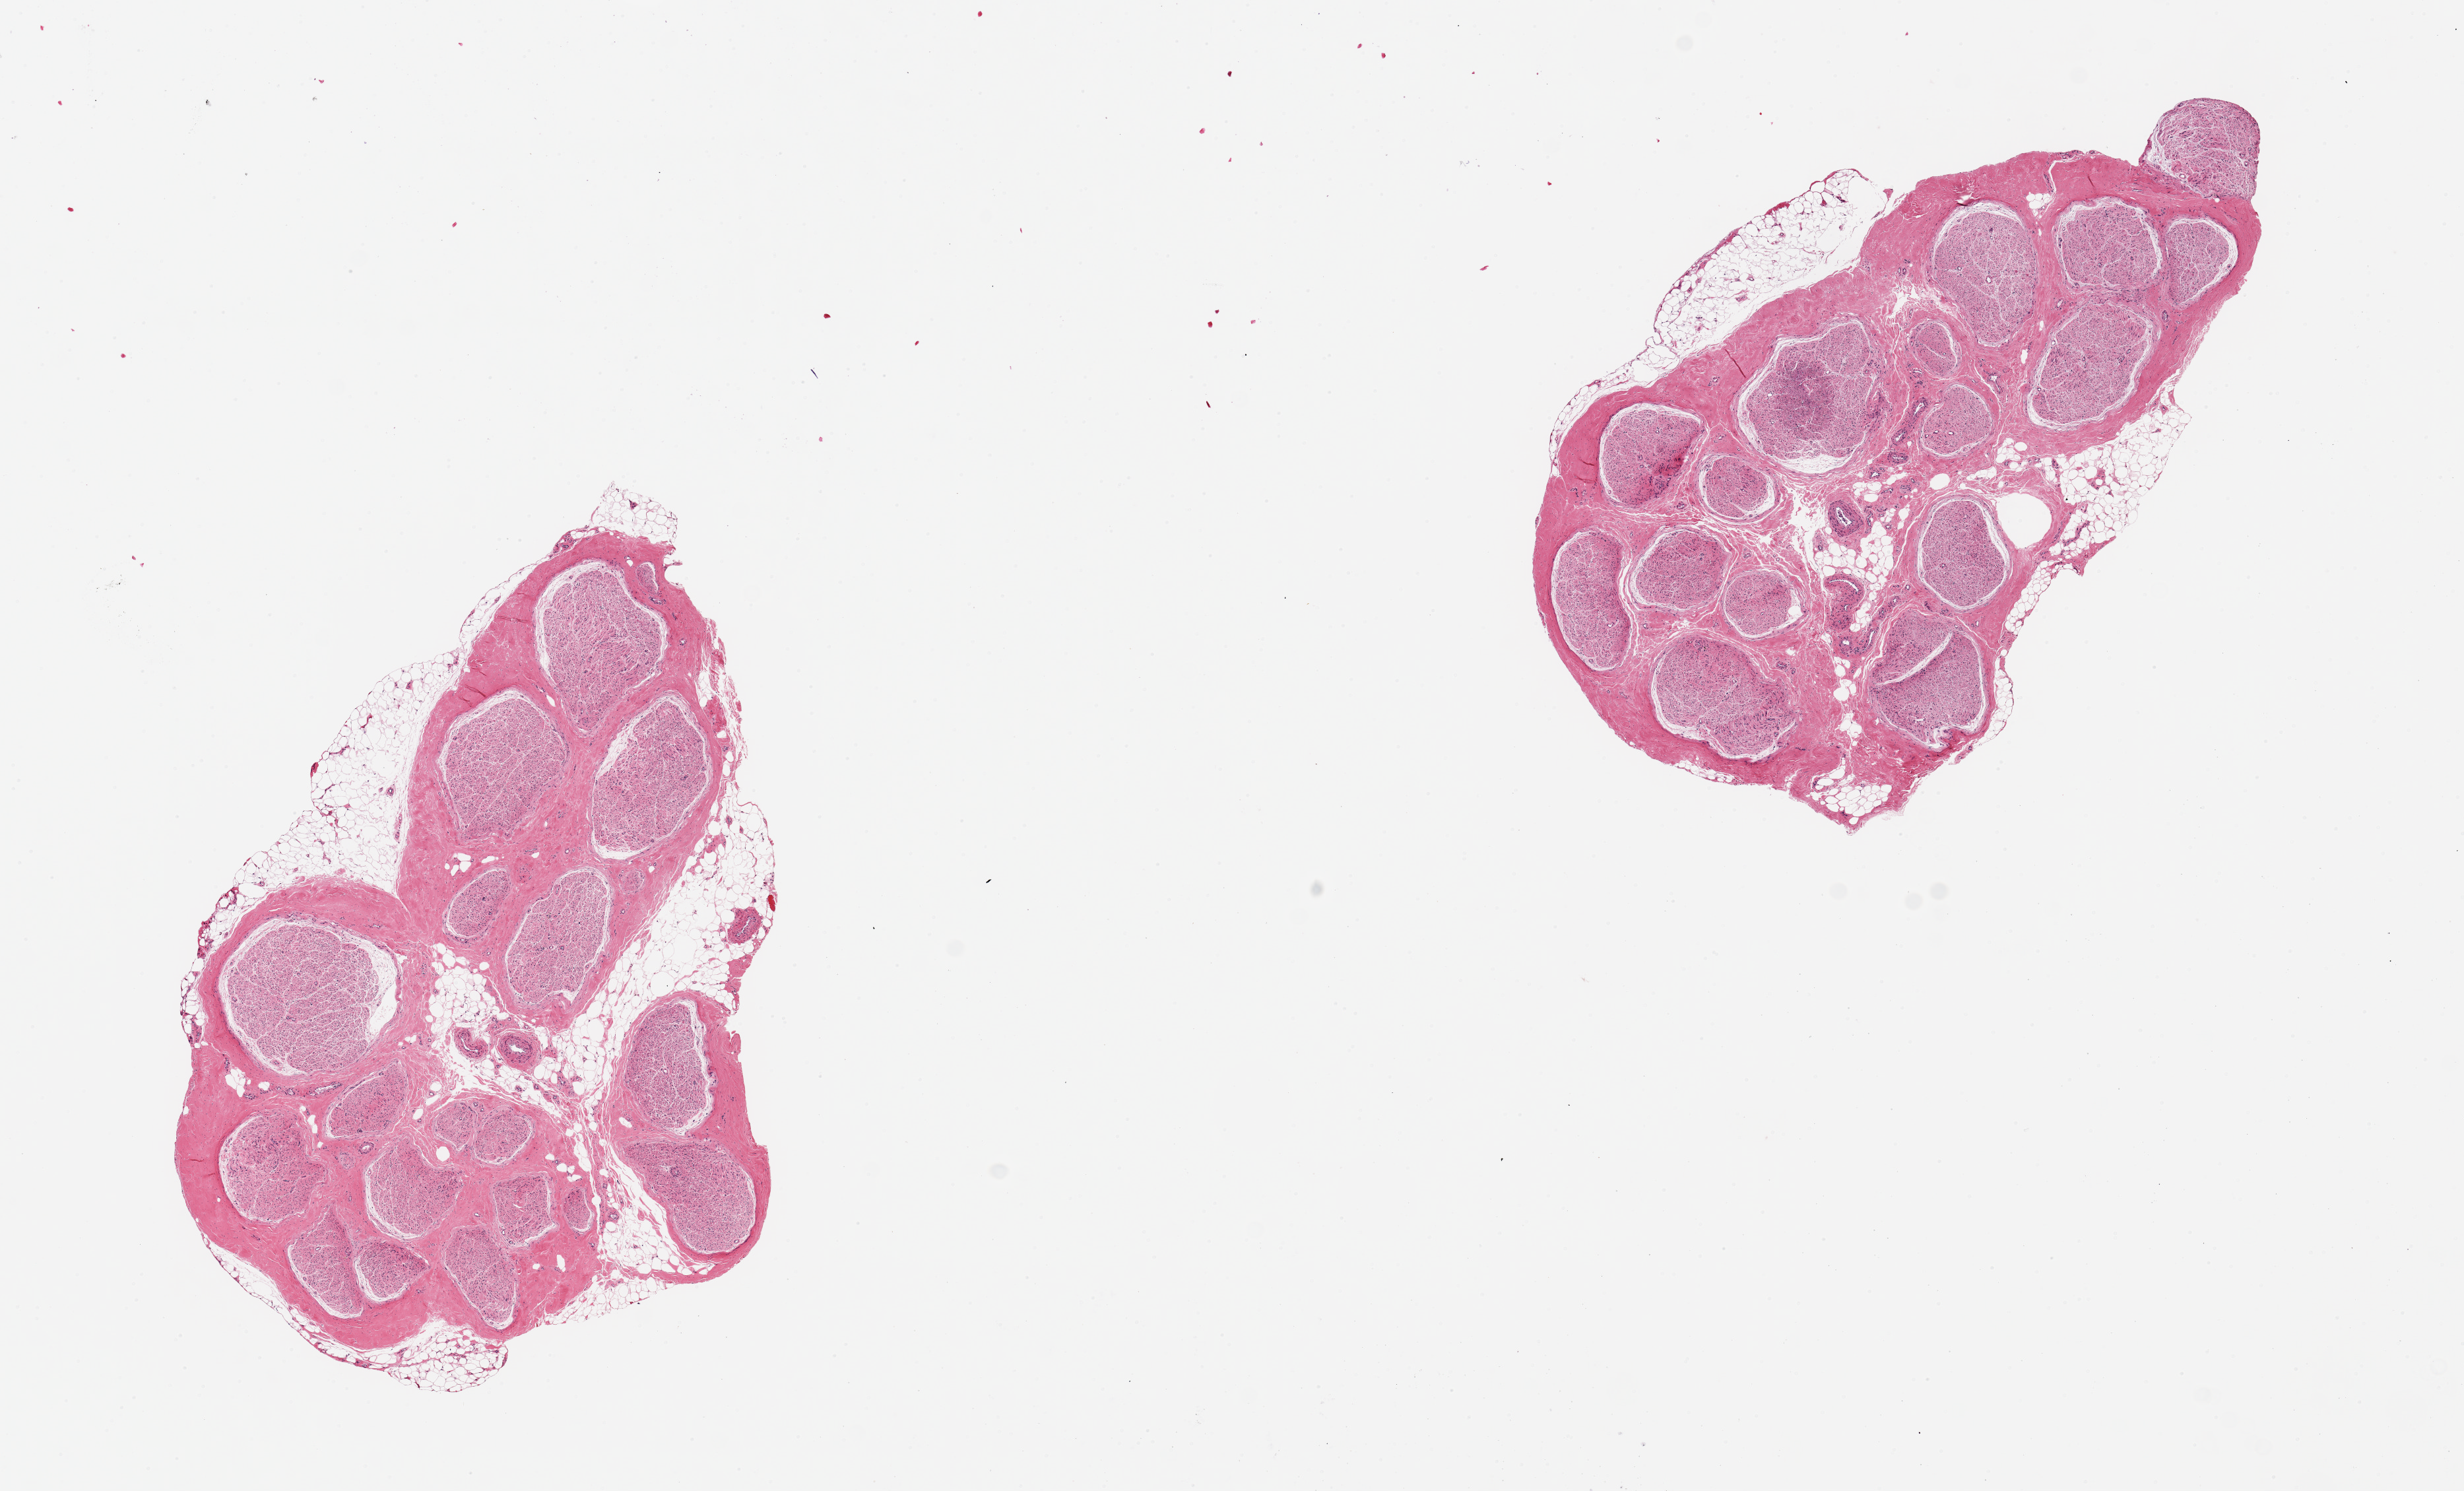
Digitized haematoxylin and eosin-stained section — low-resolution overview of the scanned area, about 14.8 x 8.9 mm (slide scanned at 20x); PAXgene-fixed paraffin-embedded (PFPE) section; target tissue: tibial nerve; donor tissue sample.
Pathologist's review note for this sample: 2 pieces 5.5x4 & 5x3mm; gnerally clean specimens, focal 0.5mm adherent nubbing of fat on one adlquot.